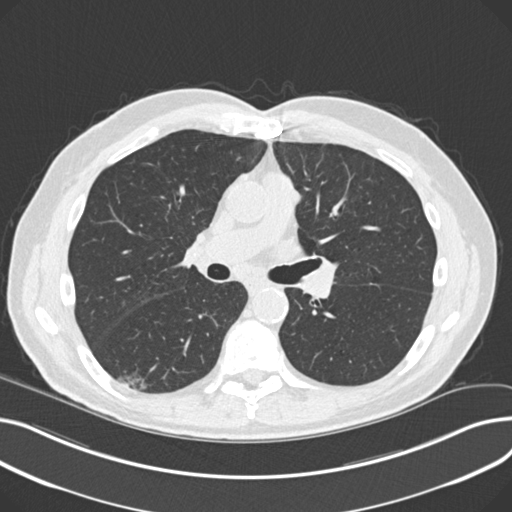
Chest CT (low-dose screening protocol), one axial image. Third annual screen. Lung window (W 1500 / L -600 HU). 2 mm slice thickness. Standard (soft-tissue) reconstruction kernel (B30f). 120 kVp. Male, age 68 years at enrolment. Current smoker at enrolment.
Lesion marked by an expert reader, bounding box [x1, y1, x2, y2] px = [122, 366, 161, 398]. The screening reader recorded 5 non-calcified nodules or masses ≥4 mm on this exam (right upper lobe, left upper lobe, right upper lobe, right lower lobe, right upper lobe); which of them this box marks is not recorded. Official screen result: positive, other. Lung cancer was diagnosed 247 days after this screen: non-small cell carcinoma, right lower lobe, poorly differentiated (G3), stage IA (AJCC 6th edition), 23 mm at pathology.